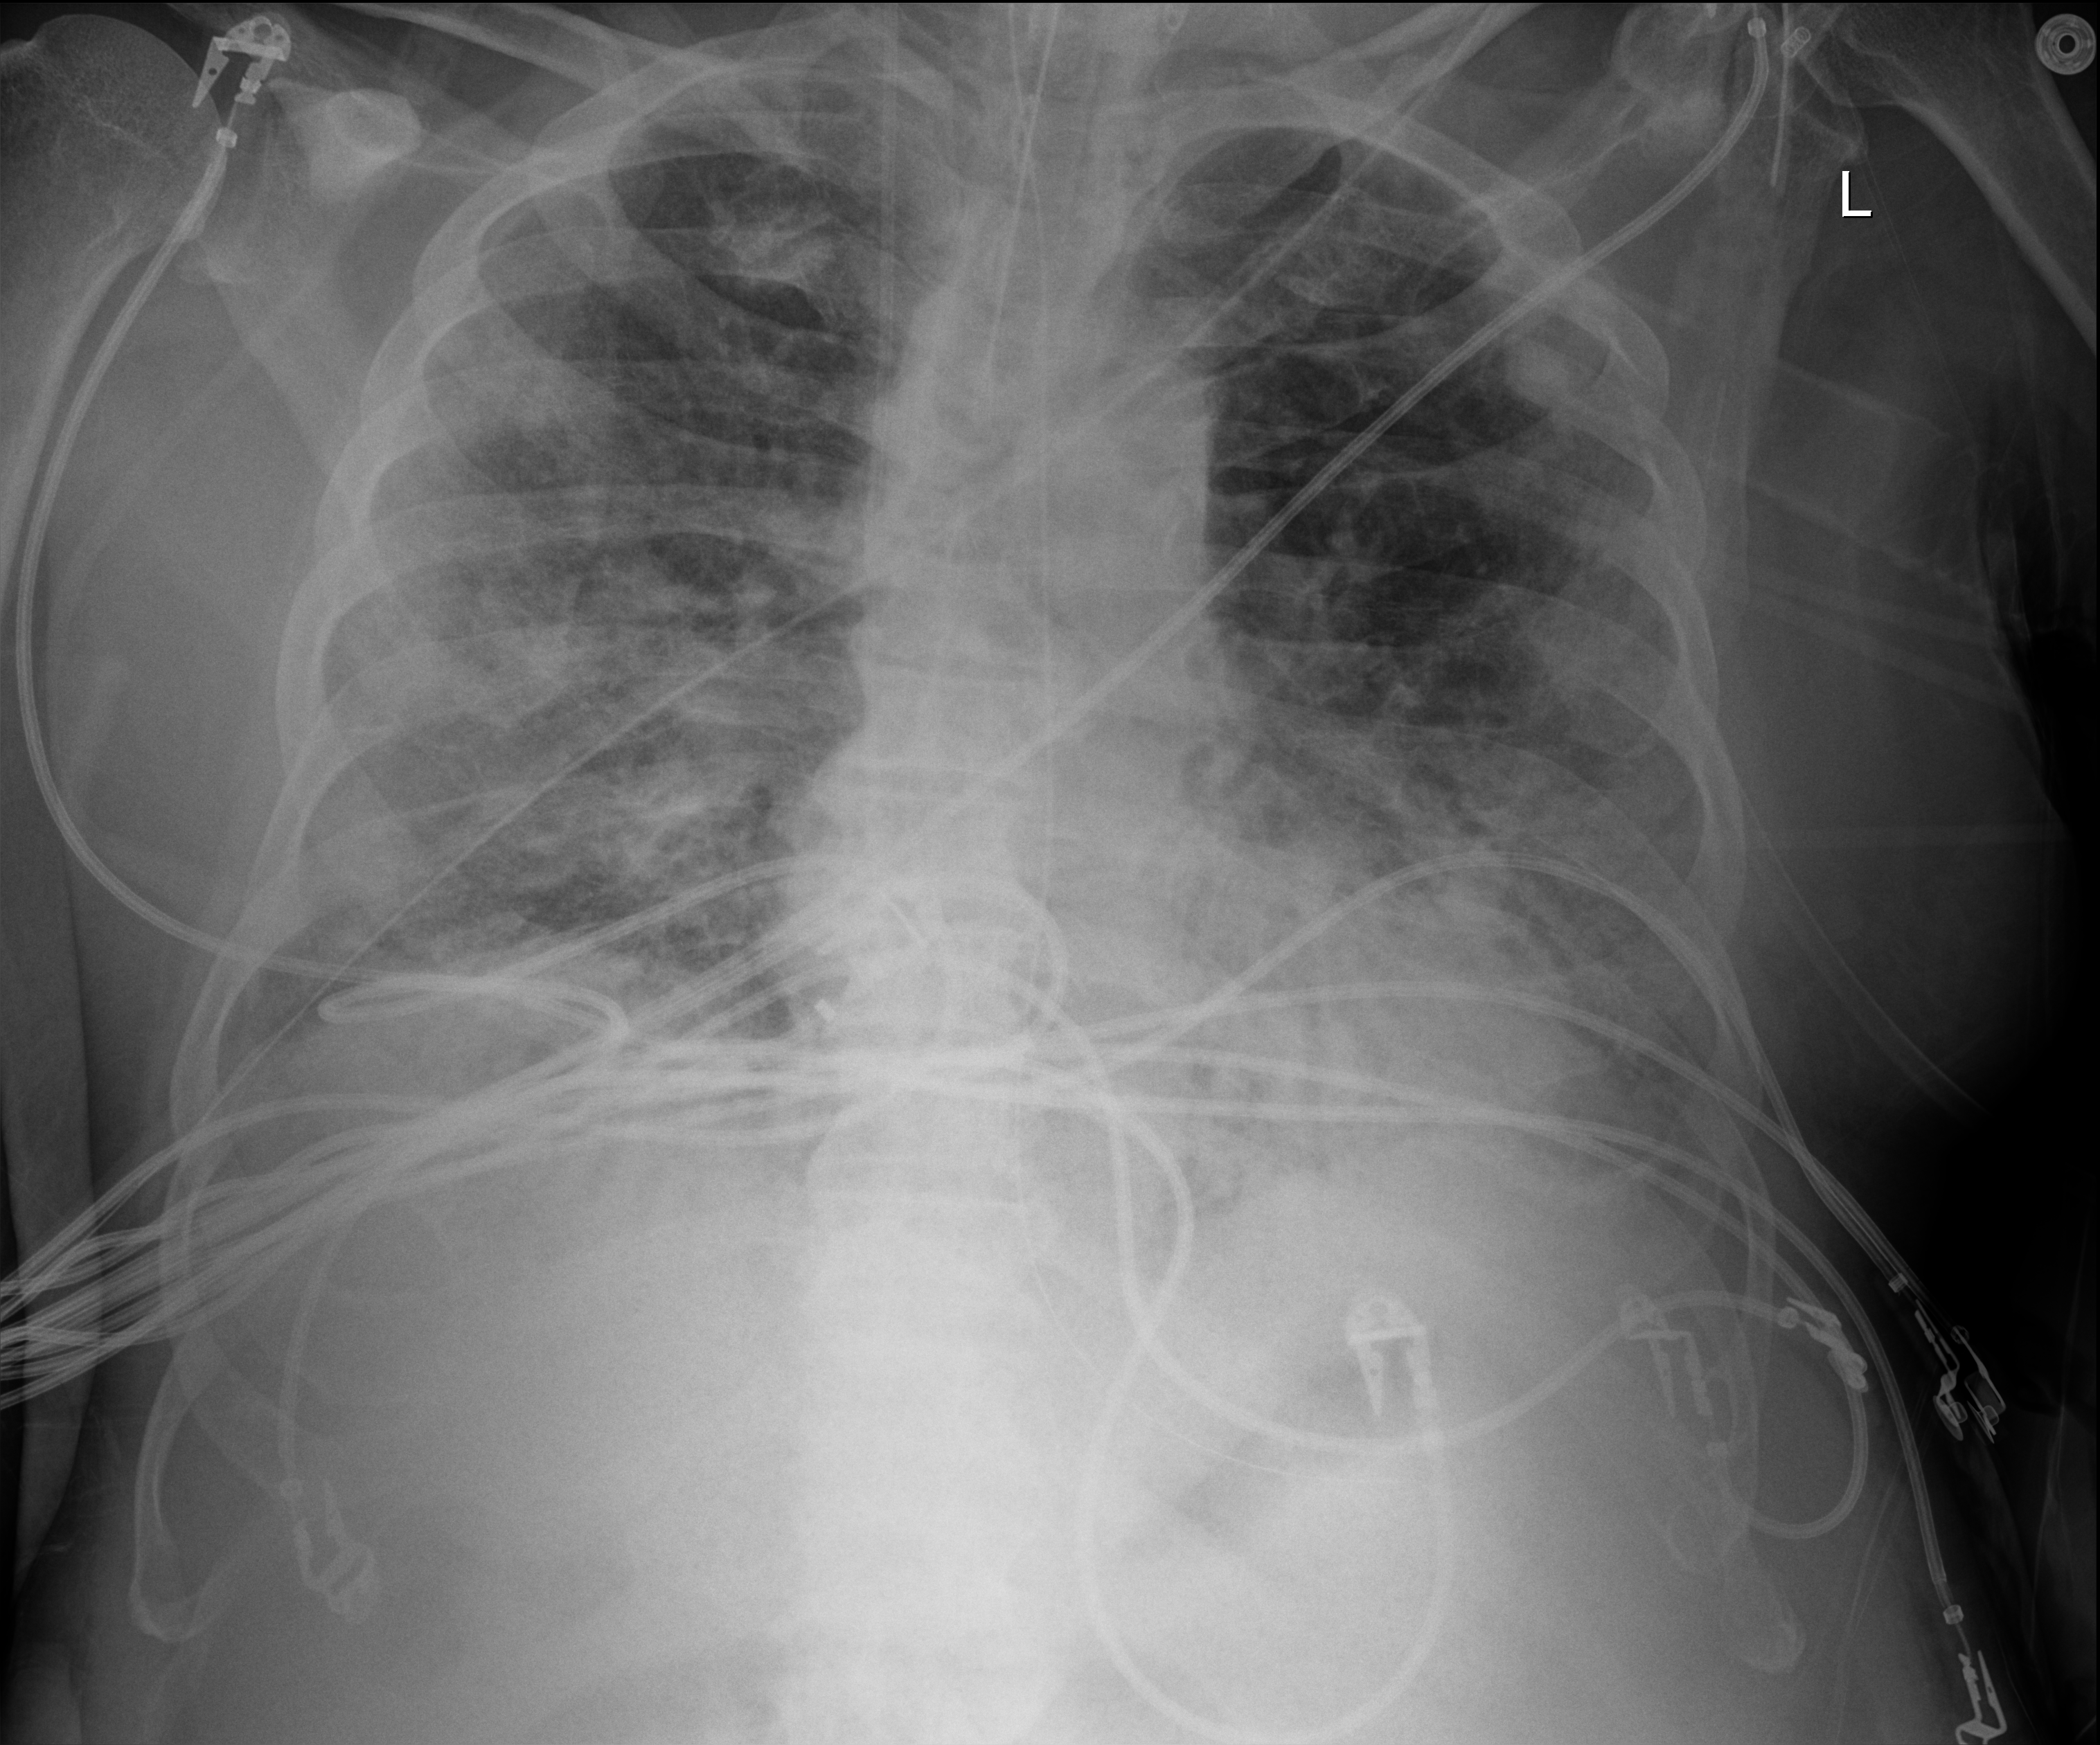
Chest radiograph (digital radiography); anteroposterior (AP) projection. Male patient hospitalised with COVID-19, age 75–90 years.
Hospital-stay facts (about this admission, not read from this image; timing relative to this image not recorded): mechanically ventilated during this hospital stay: yes; admitted to intensive care during this hospital stay: yes.